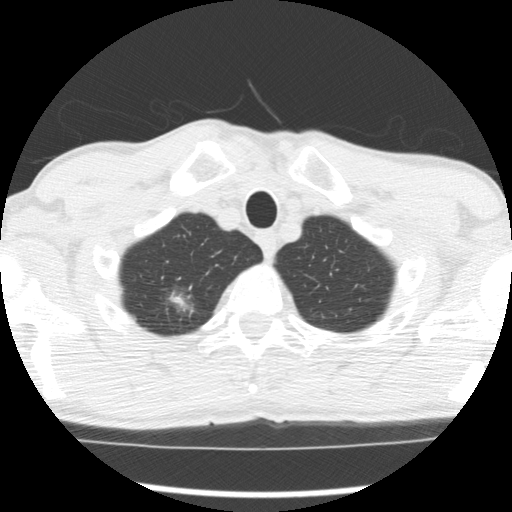
Axial slice from a low-dose chest CT screening exam, first (baseline) screen, lung window (W 1500 / L -600 HU), 2.5 mm slice thickness. Male participant, aged 66 years at enrolment. Former smoker at enrolment.
• Lesion marked by an expert reader, bounding box [x1, y1, x2, y2] px = [152, 283, 202, 330].
• The screening reader recorded 4 non-calcified nodules or masses ≥4 mm on this exam (right upper lobe, right upper lobe, right upper lobe, left lower lobe); which of them this box marks is not recorded.
• Later outcome: lung cancer diagnosed 503 days after this screen (after the second annual screen) — adenocarcinoma, NOS, right upper lobe, undifferentiated (G4), stage IA (AJCC 6th edition), 20 mm at pathology.